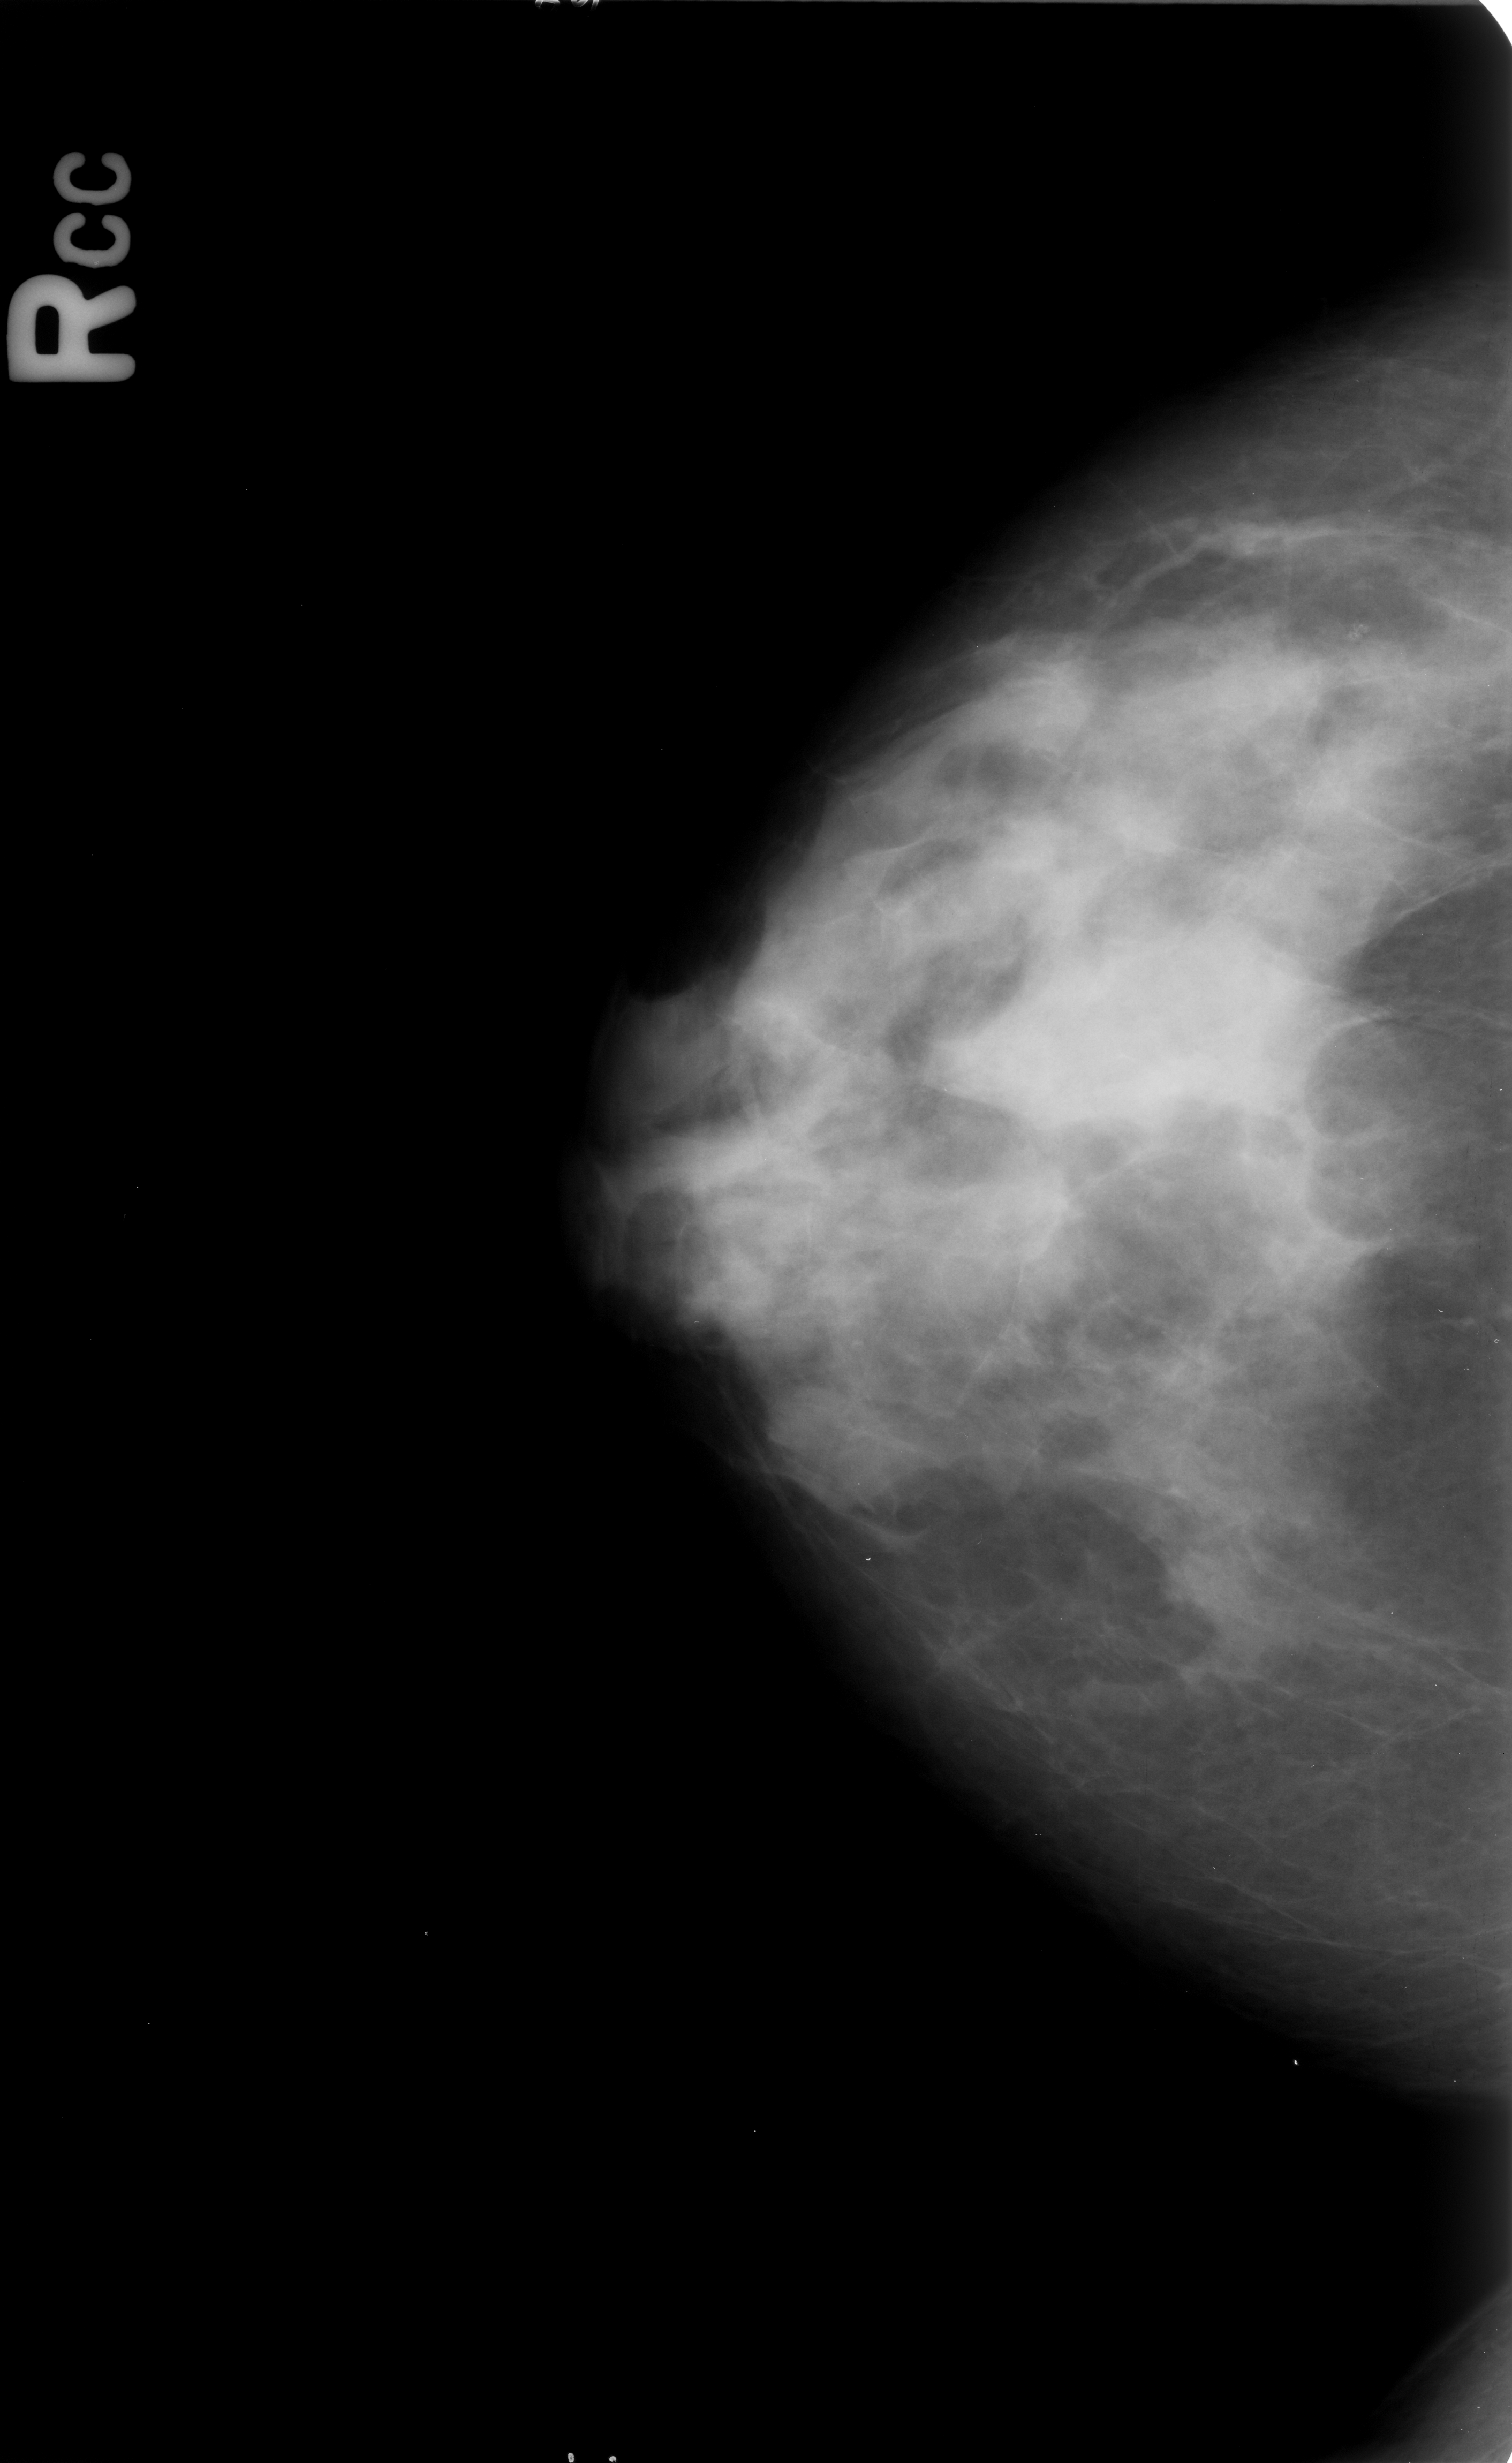
Scanned film-screen mammogram. Right breast. Craniocaudal (CC) view. BI-RADS breast density category 3 (scale 1–4). 1512 × 2463 image matrix.
Expert-marked regions of interest on this film, with their recorded descriptors:
- calcifications, morphology amorphous / pleomorphic, distribution clustered; BI-RADS assessment category 4; pathology (as recorded): benign: bounding box <1314,591,1397,686> (left, top, right, bottom; pixels)